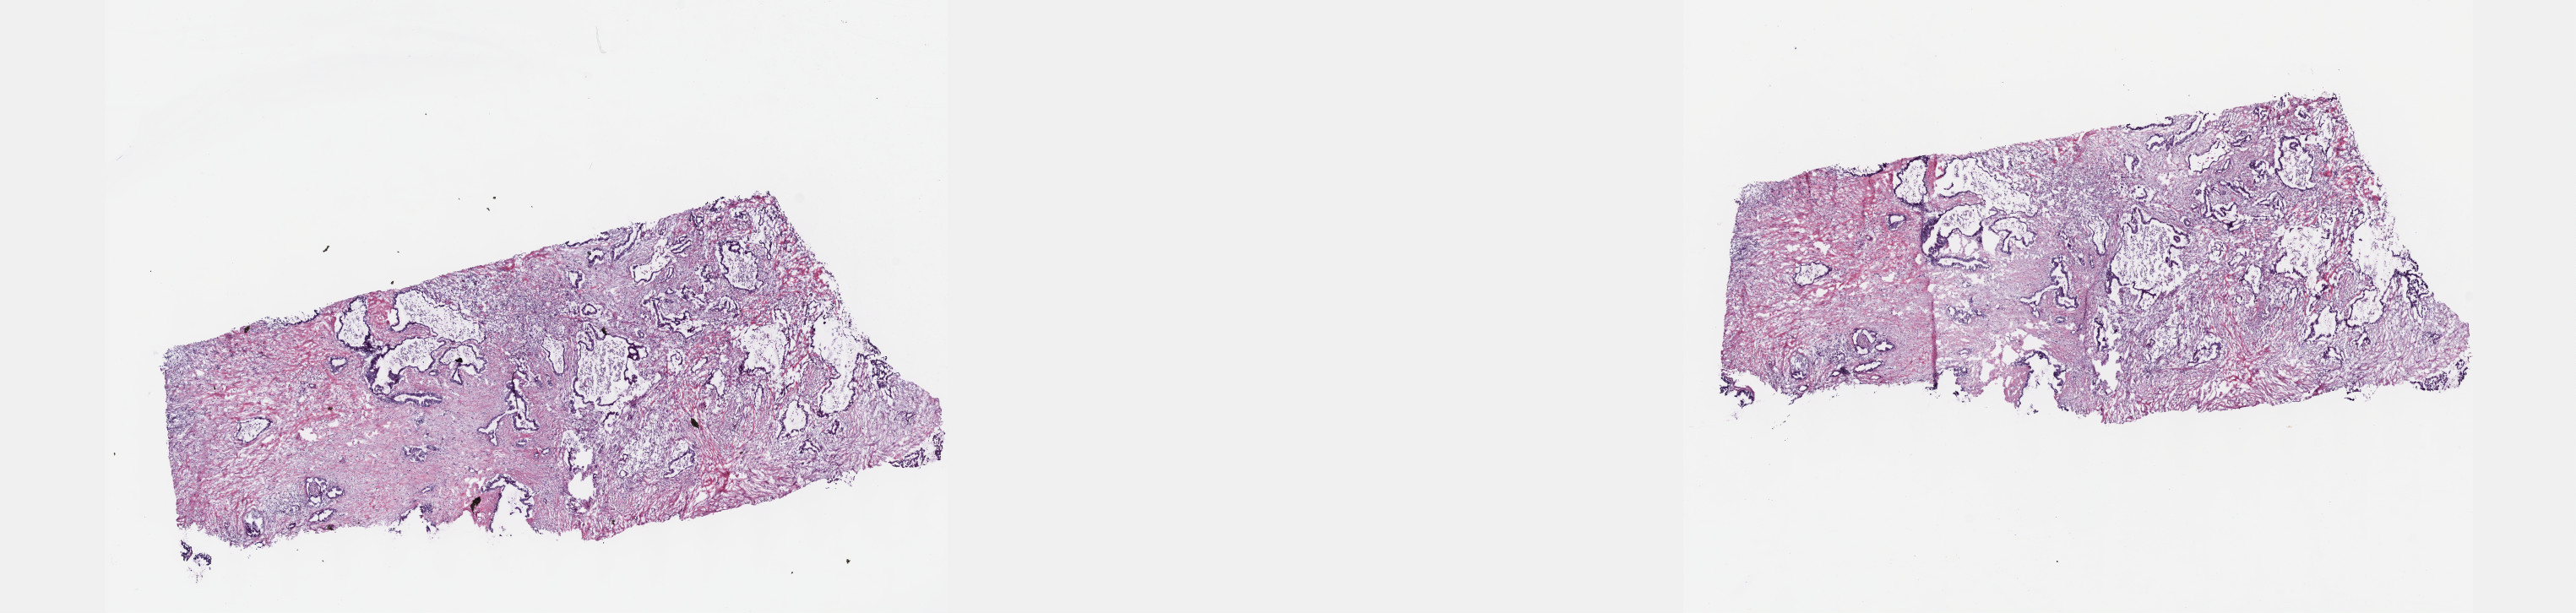
Whole-slide histology image, H&E-stained, low-resolution overview of the scanned area, about 24.6 x 5.9 mm (slide scanned at 40x). Frozen section from the top of the tissue portion. Sample: primary tumour, pancreas. Male, age 71 years at initial diagnosis.
Diagnosis: Infiltrating duct carcinoma, NOS (head of pancreas).